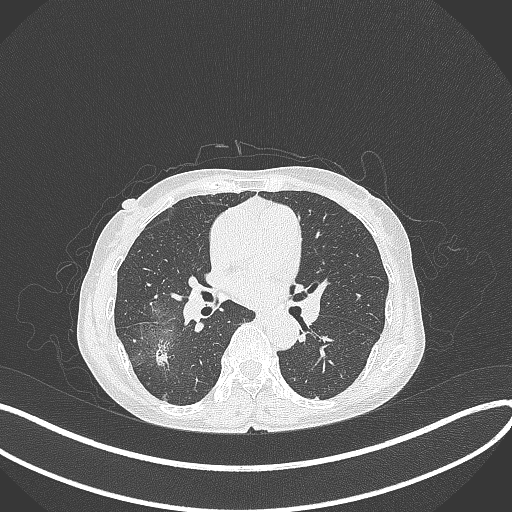
Chest CT, one axial slice. Slice 207 of 371 in the series (ordered by position). 120 kVp. Lung window (W 1500 / L -600 HU). 1 mm slice thickness. 512 × 512 image matrix, field of view 400 × 400 mm. Female patient, age 69 years. From the clinical record (not read from this slice): clinical TNM (as recorded): T1b N0 M0; histopathological grade: G2-3.
Structures marked on this image (bounding box drawn by a radiologist):
- lung tumour (recorded histology: adenocarcinoma): box from (x=148, y=332) to (x=177, y=375) px